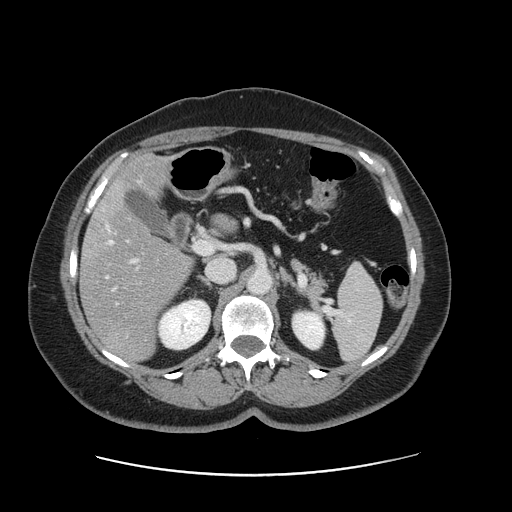
Contrast-enhanced abdominal CT, one axial slice. Position 79 of 161 along the scan axis. Soft-tissue window (W 400 / L 40 HU). 512 × 512 image matrix, field of view 398 × 398 mm. Female patient, age 62 years. From the clinical record (not read from this slice): diagnosis: colorectal cancer liver metastases, imaged before liver resection; multiple liver metastases: no; largest metastasis: 2.5 cm; chemotherapy before resection: yes.
Outlined on this slice (expert manual segmentation):
- hepatic veins: bounding box <106,180,141,290> (left, top, right, bottom; pixels)
- liver: <81,156,192,362>
- planned liver remnant (the part of the liver to remain after resection): <114,156,166,194>
- portal vein (with intrahepatic branches): <127,241,137,263>